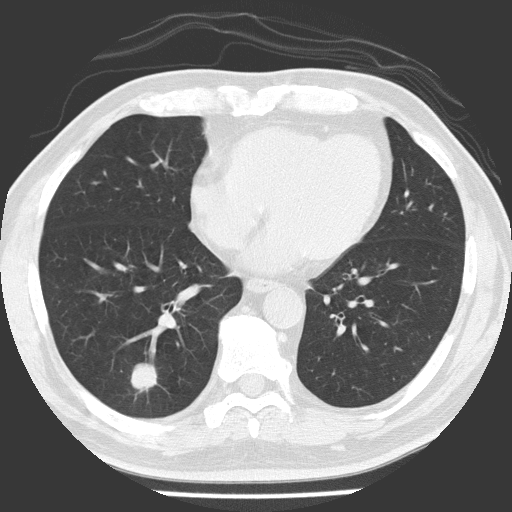
Chest CT (low-dose screening protocol), one axial image, baseline annual screen, lung window (W 1500 / L -600 HU), lung (sharp) reconstruction kernel (FC51). Male participant, aged 56 years at enrolment.
Lesion marked by an expert reader, bounding box [x1, y1, x2, y2] px = [110, 347, 165, 404]. Screening reader's record for this exam (one nodule recorded; not confirmed to be the boxed lesion): non-calcified nodule or mass ≥4 mm, right lower lobe, 21 × 17 mm, spiculated (stellate) margins, soft tissue attenuation. Official screen result: positive, change unspecified: nodule(s) >= 4 mm or enlarging nodule(s), mass(es), or other non-specific abnormalities suspicious for lung cancer. Participant outcome: lung cancer diagnosed 84 days after this screen — adenocarcinoma, NOS, right lower lobe, poorly differentiated (G3), stage IA (AJCC 6th edition), 24 mm at pathology.